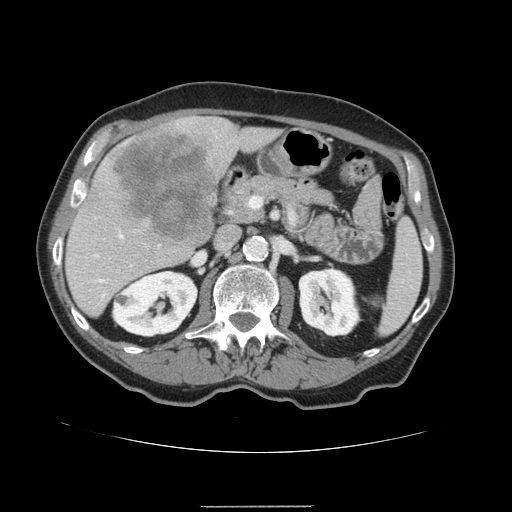
Contrast-enhanced abdominal CT, one axial slice. Position 74 of 168 along the scan axis. Intravenous contrast given. Soft-tissue window (W 400 / L 40 HU). 2.5 mm slice thickness. 512 × 512 image matrix, field of view 386 × 386 mm. Male patient, age 74 years. Case-level facts recorded for this patient, not image findings: diagnosis: colorectal cancer liver metastases, imaged before liver resection; multiple liver metastases: no; largest metastasis: 14.5 cm; disease in both lobes: yes.
Outlined on this slice (manually delineated by an expert):
- liver: bounding box <65,116,283,318> (left, top, right, bottom; pixels)
- planned liver remnant (the part of the liver to remain after resection): <66,126,282,318>
- liver metastasis: <112,124,219,247>